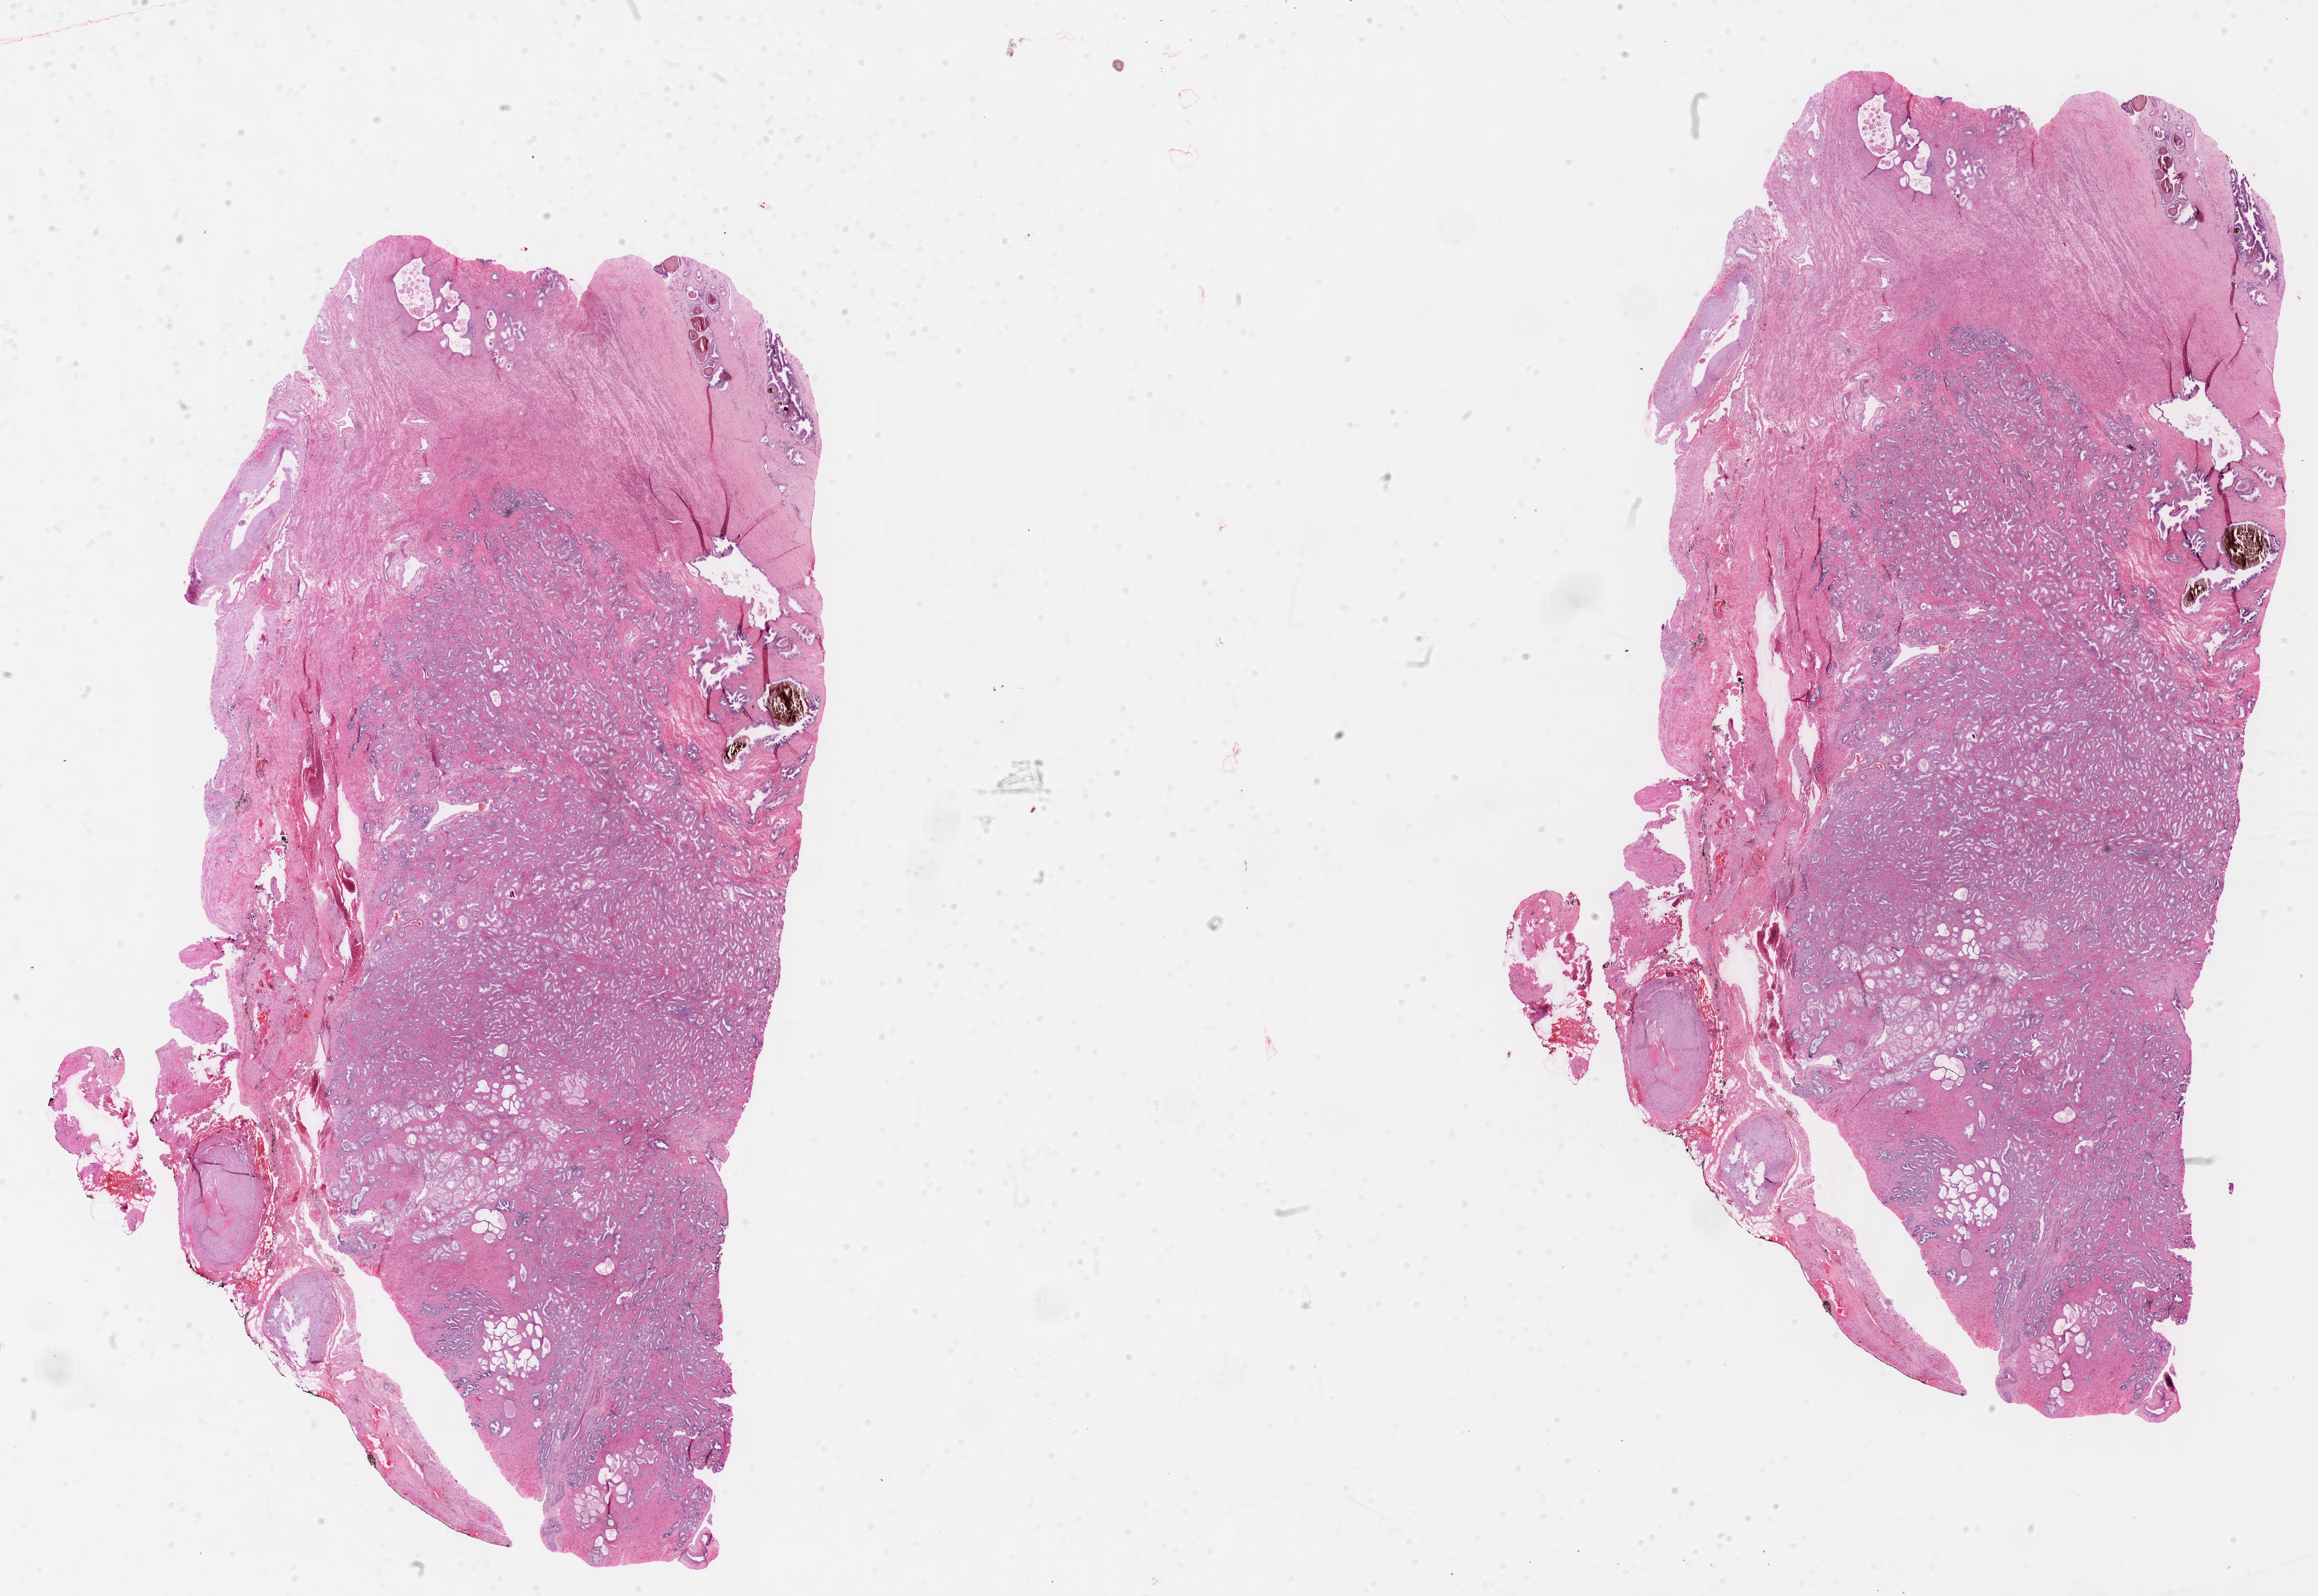
H&E whole-slide image, shown as a low-resolution overview of the whole scanned area (about 30.2 x 20.8 mm). FFPE section. Prostate, primary tumour sample. Male patient; age at initial diagnosis 66 years. Gleason score: 6 (3+3).
Diagnosis: Adenocarcinoma, NOS (prostate gland). Laterality: right.